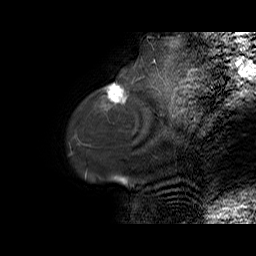
Breast MRI (dynamic contrast-enhanced), one sagittal slice. Slice 10 of 70 in the series (ordered by position). Dynamic contrast-enhanced series, time point 2 of 6 at this slice position (early post-contrast). 1.5 T. TE 5.5 ms, TR 32.9 ms. 4 mm slice thickness. 256 × 256 image matrix, field of view 240 × 240 mm. Female patient. From the clinical record (not read from this slice): setting: breast cancer imaged before/during neoadjuvant chemotherapy; receptor status: HER2-positive.
Annotated regions visible in this slice (semi-automatic segmentation, software-assisted and operator-edited):
- analysis volume of interest (the breast-tissue region the enhancement analysis was run in; not a lesion): bounding box [x1, y1, x2, y2] px = [98, 80, 141, 106]
- tumour enhancement mask (voxels above the 100 % enhancement threshold inside the analysis volume of interest): [107, 83, 127, 103]